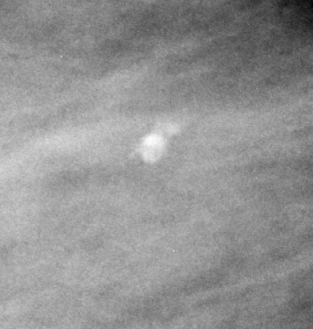
Crop from a digitized film mammogram around one marked abnormality, right breast, MLO view, BI-RADS breast density category 4 (scale 1–4).
- Marked abnormality: calcifications, morphology dystrophic, distribution clustered; BI-RADS assessment category 3; subtlety rating 5 on a 1 (subtle) to 5 (obvious) scale; pathology result (as recorded, not read from the image): benign.